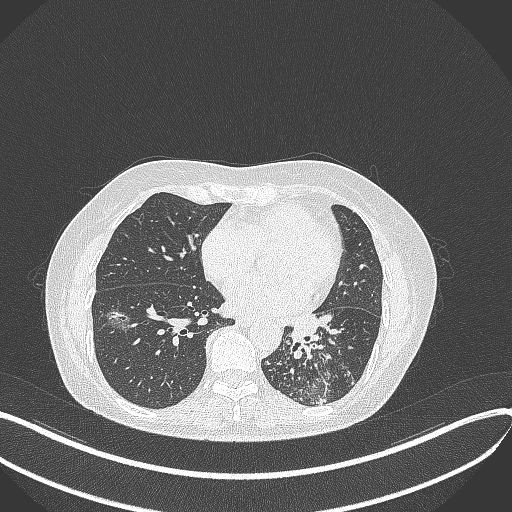
Chest CT, one axial slice. Position 165 of 429 along the scan axis. Reconstruction kernel B70f. 100 kVp. Lung window (W 1500 / L -600 HU). 1 mm slice thickness. 512 × 512 image matrix, field of view 400 × 400 mm. Female patient, age 63 years. From the clinical record (not read from this slice): clinical TNM (as recorded): T1b N0 M0.
Annotated regions visible in this slice (rectangle marked by the reading radiologist):
- lung tumour (recorded histology: adenocarcinoma): bounding box [x1, y1, x2, y2] px = [283, 311, 323, 347]